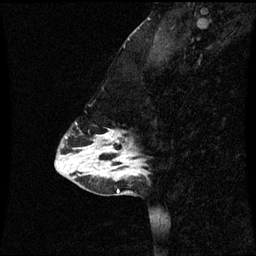
Breast MRI (dynamic contrast-enhanced), one sagittal slice. Position 20 of 60 along the scan axis. Dynamic contrast-enhanced series, image 2 of 3 at this slice position (ordered by acquisition). 1.5 T. TE 4.2 ms, TR 8.9 ms. 2 mm slice thickness. 256 × 256 image matrix, field of view 220 × 220 mm. Female patient, age 43 years. From the clinical record (not read from this slice): setting: breast cancer imaged before/during neoadjuvant chemotherapy; receptor status: HR-positive, HER2-negative.
Outlined on this slice (semi-automatically segmented with operator editing):
- analysis volume of interest (the breast-tissue region the enhancement analysis was run in; not a lesion): bounding box <84,134,144,171> (left, top, right, bottom; pixels)
- tumour enhancement mask (voxels above the 70 % enhancement threshold inside the analysis volume of interest): <104,134,125,159>